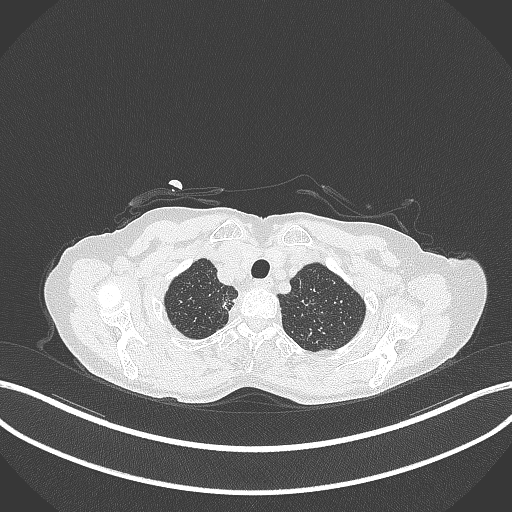
Chest CT, one axial slice. Position 335 of 403 along the scan axis. 120 kVp. Lung window (W 1500 / L -600 HU). 1 mm slice thickness. 512 × 512 image matrix, field of view 400 × 400 mm. Female patient, age 75 years. From the clinical record (not read from this slice): clinical TNM (as recorded): T1c N1 M1.
Outlined on this slice (bounding box drawn by a radiologist):
- lung tumour (recorded histology: adenocarcinoma): box from (x=219, y=286) to (x=245, y=314) px